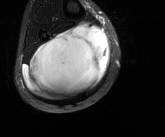
MRI of an extremity soft-tissue mass, one axial slice; position 61 of 81 along the scan axis; T2-weighted fat-saturated; MR volume resampled by the dataset authors to the PET/CT grid (not the native acquisition matrix); 165 × 137 image matrix, field of view 161 × 134 mm. Male patient. Case-level facts recorded for this patient, not image findings: histological type: liposarcoma - round cell; grade: high; site of the primary tumour: right calf.
Structures marked on this image (expert contour drawn on MRI and transferred to this co-registered scan by the dataset authors):
- gross tumour volume (mass): bounding box [x1, y1, x2, y2] px = [23, 23, 111, 101]